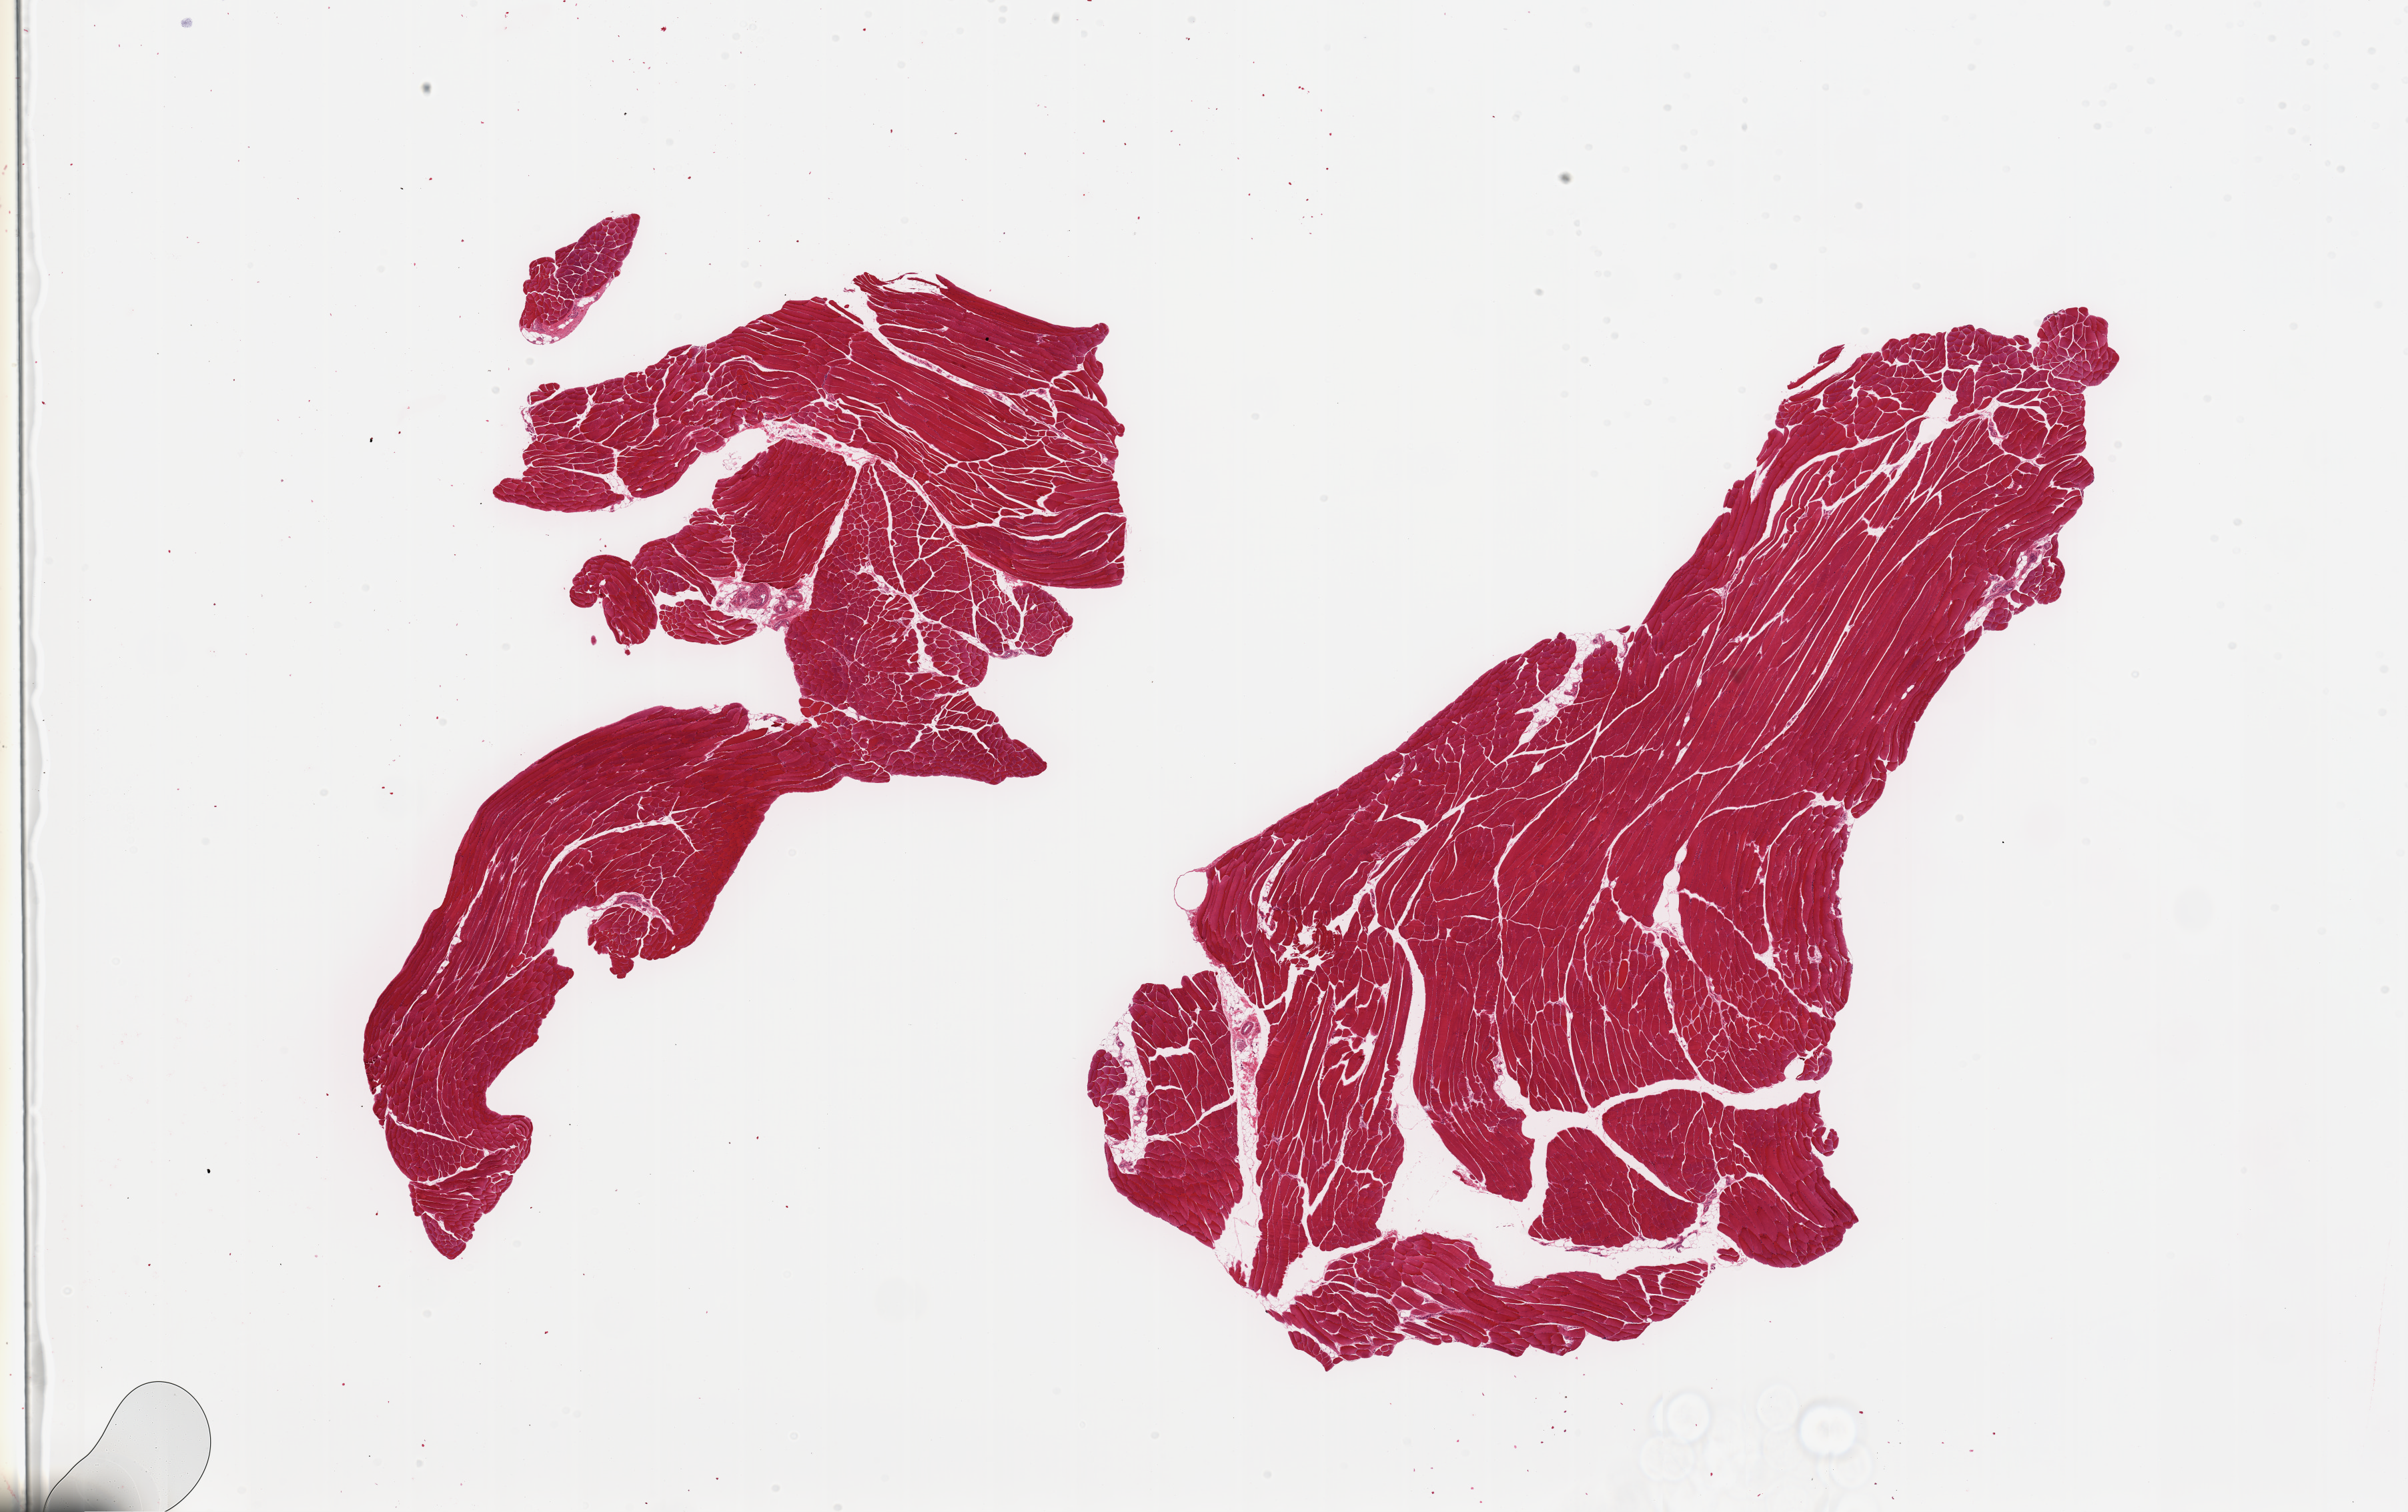
Digitized haematoxylin and eosin-stained section, brightfield — shown as a low-resolution overview of the whole scanned area (about 28.5 x 17.9 mm), PAXgene-fixed paraffin-embedded (PFPE) section, target tissue: skeletal muscle, tissue donor sample.
Review note (as recorded): 2 pieces, only trace interstitial fat.